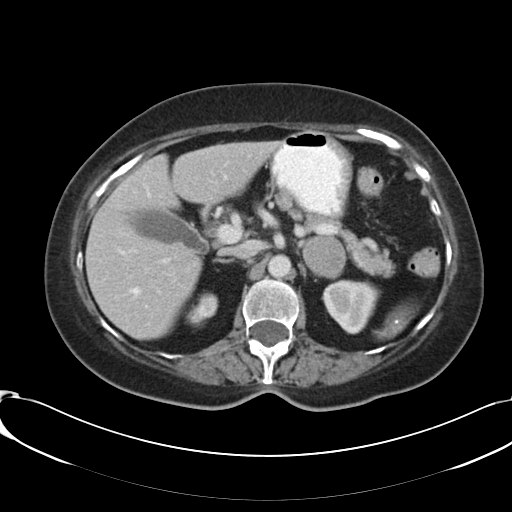
Contrast-enhanced abdominal CT, one axial slice; slice 69 of 91 in the series (ordered by position); intravenous contrast given; soft-tissue window (W 400 / L 40 HU); 5 mm slice thickness; 512 × 512 image matrix, field of view 366 × 366 mm. Female patient, age 73 years. From the clinical record (not read from this slice): diagnosis: adrenocortical carcinoma; tumour side: left adrenal; tumour size at pathology: 4.9 cm; Ki-67 index: 10 %.
Annotated regions visible in this slice (semi-automatically segmented with operator editing):
- mass: bounding box [x1, y1, x2, y2] px = [303, 237, 344, 277]